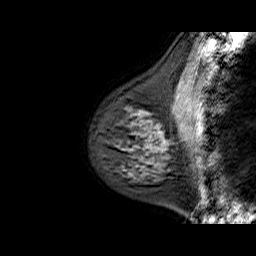
Breast MRI (dynamic contrast-enhanced), one sagittal slice. Position 19 of 60 along the scan axis. Dynamic contrast-enhanced series, time point 2 of 6 at this slice position (early post-contrast). 1.5 T. TE 6.4 ms, TR 32.9 ms. 4 mm slice thickness. 256 × 256 image matrix. Female patient. From the clinical record (not read from this slice): setting: breast cancer imaged before/during neoadjuvant chemotherapy; receptor status: HR-positive, HER2-negative.
Structures marked on this image (semi-automatically segmented with operator editing):
- analysis volume of interest (the breast-tissue region the enhancement analysis was run in; not a lesion): box from (x=104, y=94) to (x=168, y=175) px
- tumour enhancement mask (voxels above the 100 % enhancement threshold inside the analysis volume of interest): (x=158, y=132)–(x=161, y=134)